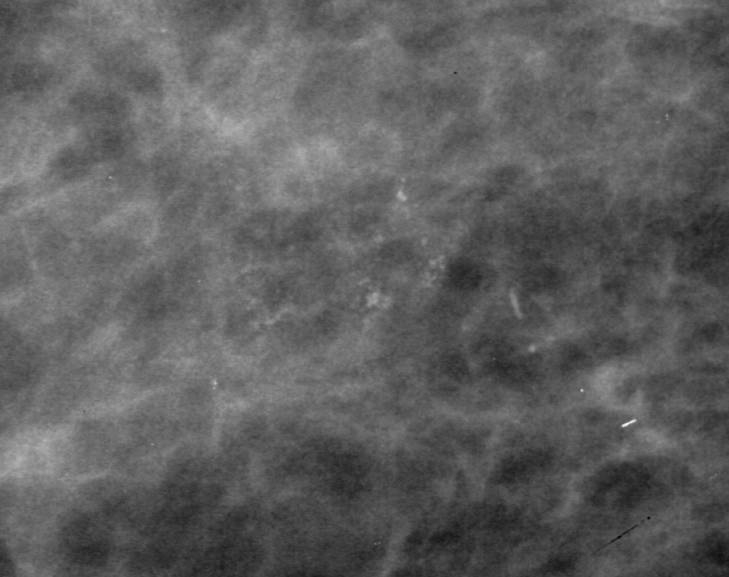
Region of interest cut from a scanned film mammogram (one marked finding), left breast, CC view.
Calcifications, morphology pleomorphic, distribution clustered; BI-RADS assessment category 4; subtlety rating 3 on a 1 (subtle) to 5 (obvious) scale; pathology result (as recorded, not read from the image): benign.